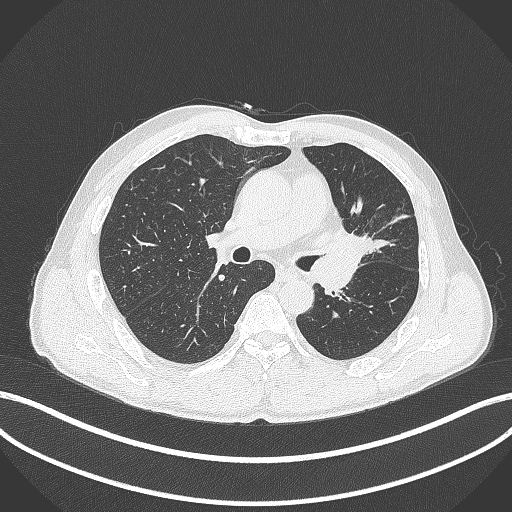
Chest CT, one axial slice. Slice 247 of 429 in the series (ordered by position). 120 kVp. Lung window (W 1500 / L -600 HU). 1 mm slice thickness. 512 × 512 image matrix, field of view 400 × 400 mm. Patient: male, 57 years. Case-level facts recorded for this patient, not image findings: clinical TNM (as recorded): T2b N0 M0.
Structures marked on this image (bounding box drawn by a radiologist):
- lung tumour (recorded histology: squamous cell carcinoma): box from (x=323, y=224) to (x=376, y=260) px